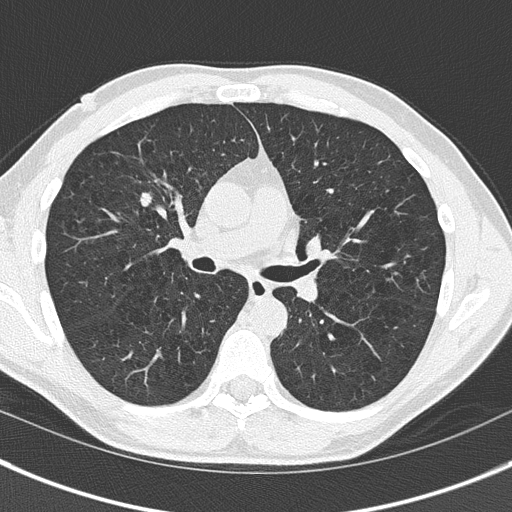
Chest CT (low-dose screening protocol), one axial image. First (baseline) screen. Lung window (W 1500 / L -600 HU). Slice 77 of 175 in the series. Male participant, aged 56 years at enrolment.
Expert-annotated lung lesion, bounding box <130,185,162,217> (left, top, right, bottom; pixels). The screening reader recorded 3 non-calcified nodules or masses ≥4 mm on this exam (right upper lobe, right upper lobe, left lower lobe); which of them this box marks is not recorded. Official screen result: positive, change unspecified: nodule(s) >= 4 mm or enlarging nodule(s), mass(es), or other non-specific abnormalities suspicious for lung cancer. Later outcome: lung cancer diagnosed 228 days after this screen — non-small cell carcinoma, right upper lobe, stage IIIA (AJCC 6th edition), 21 mm at pathology.